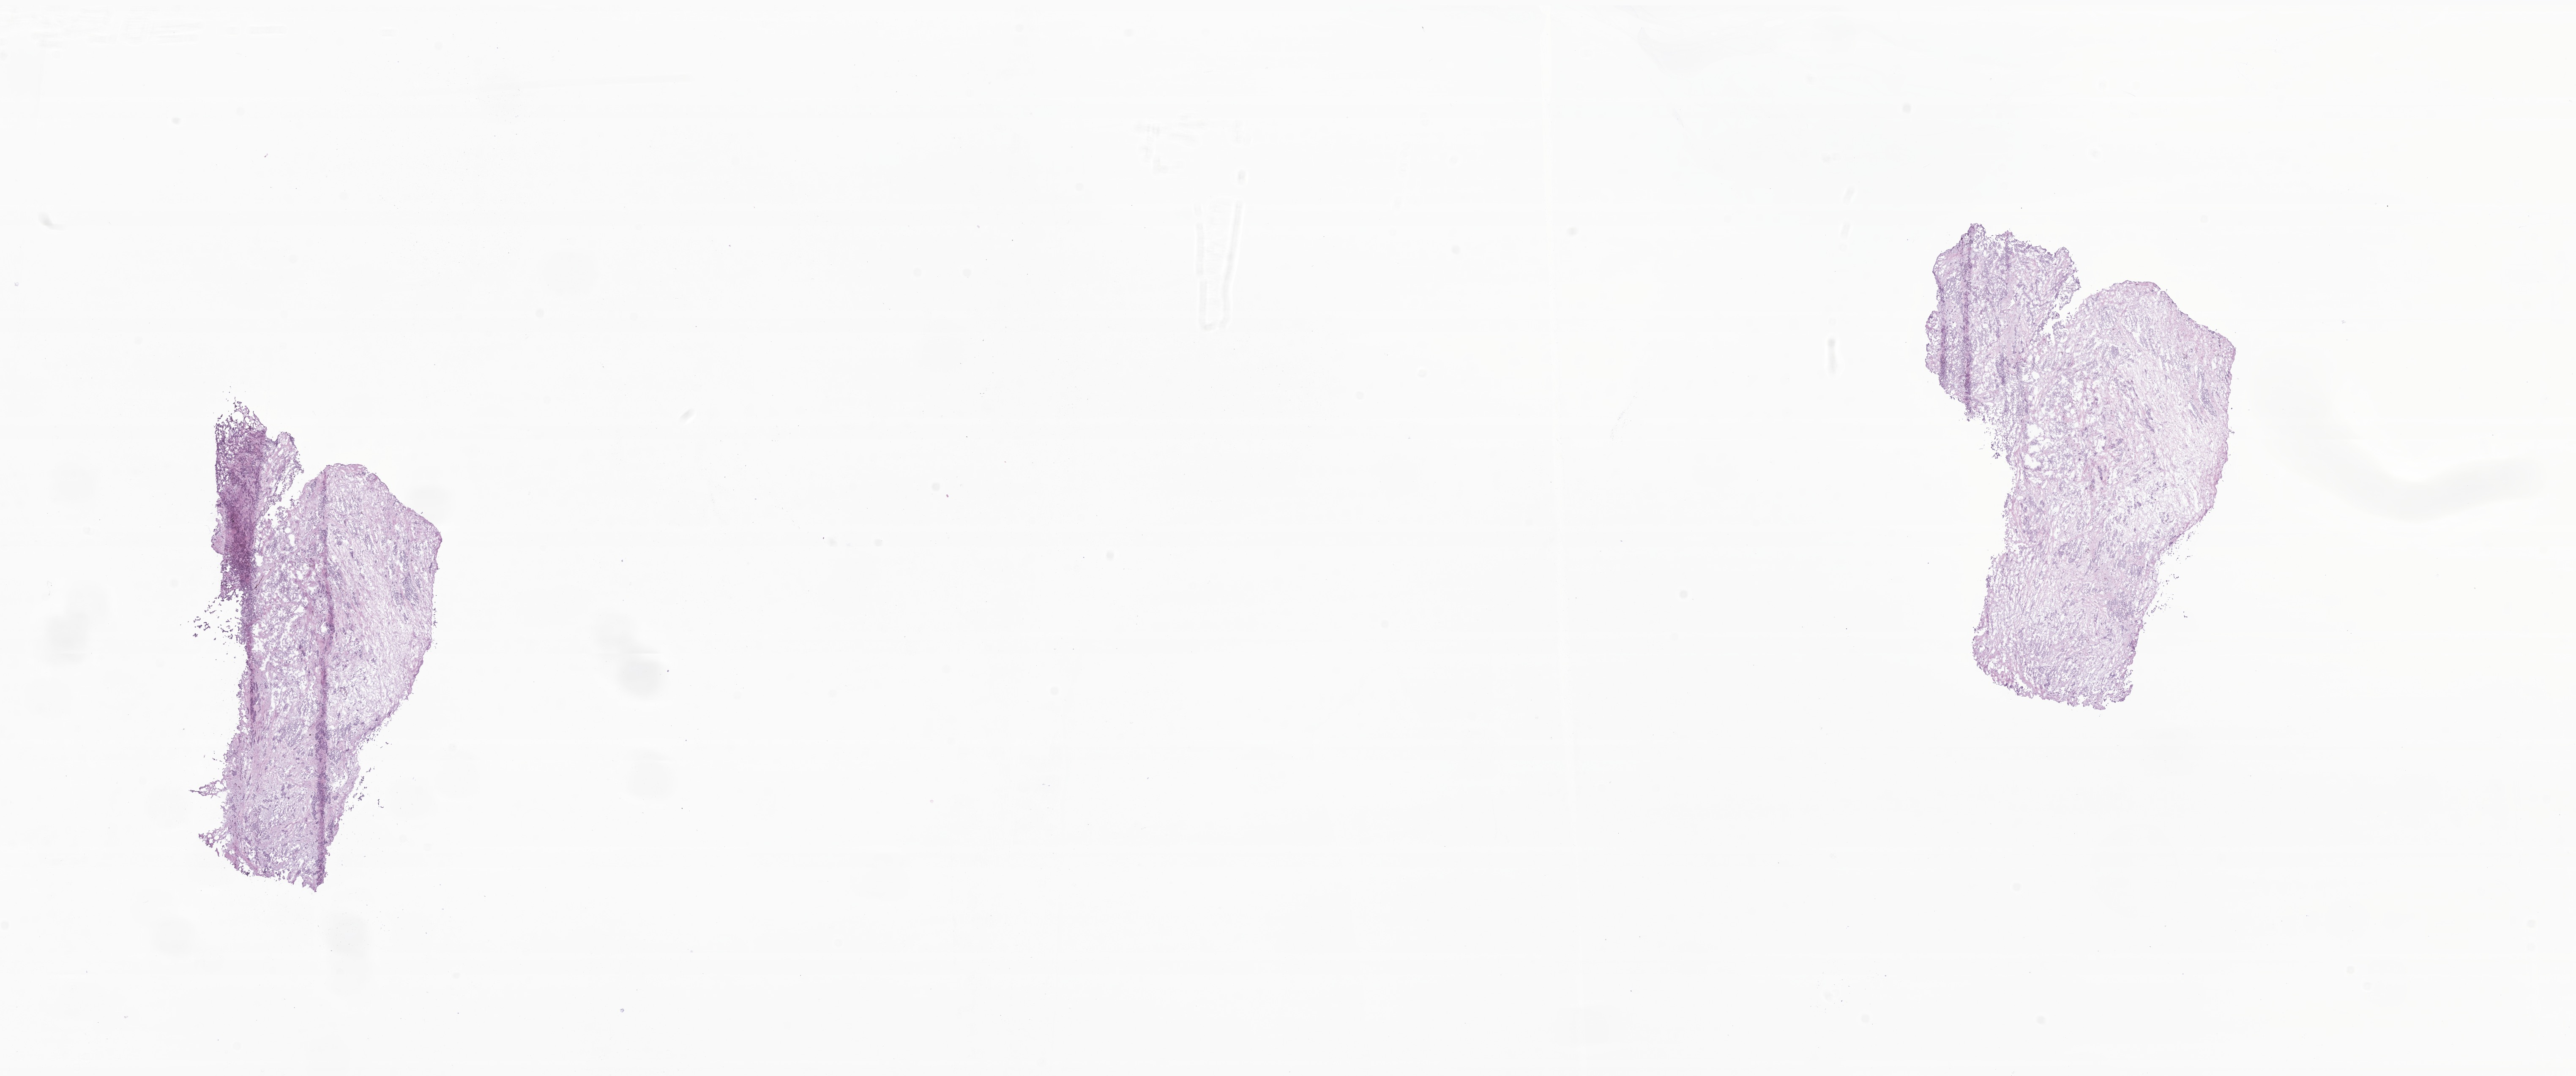
Whole-slide image, haematoxylin and eosin stain of tumor tissue from the testis — whole scanned area (about 25.7 x 10.7 mm) shown as a low-resolution overview. Frozen section (OCT-embedded). Male patient, age 157 days.
* recorded diagnosis: Embryonal rhabdomyosarcoma, NOS